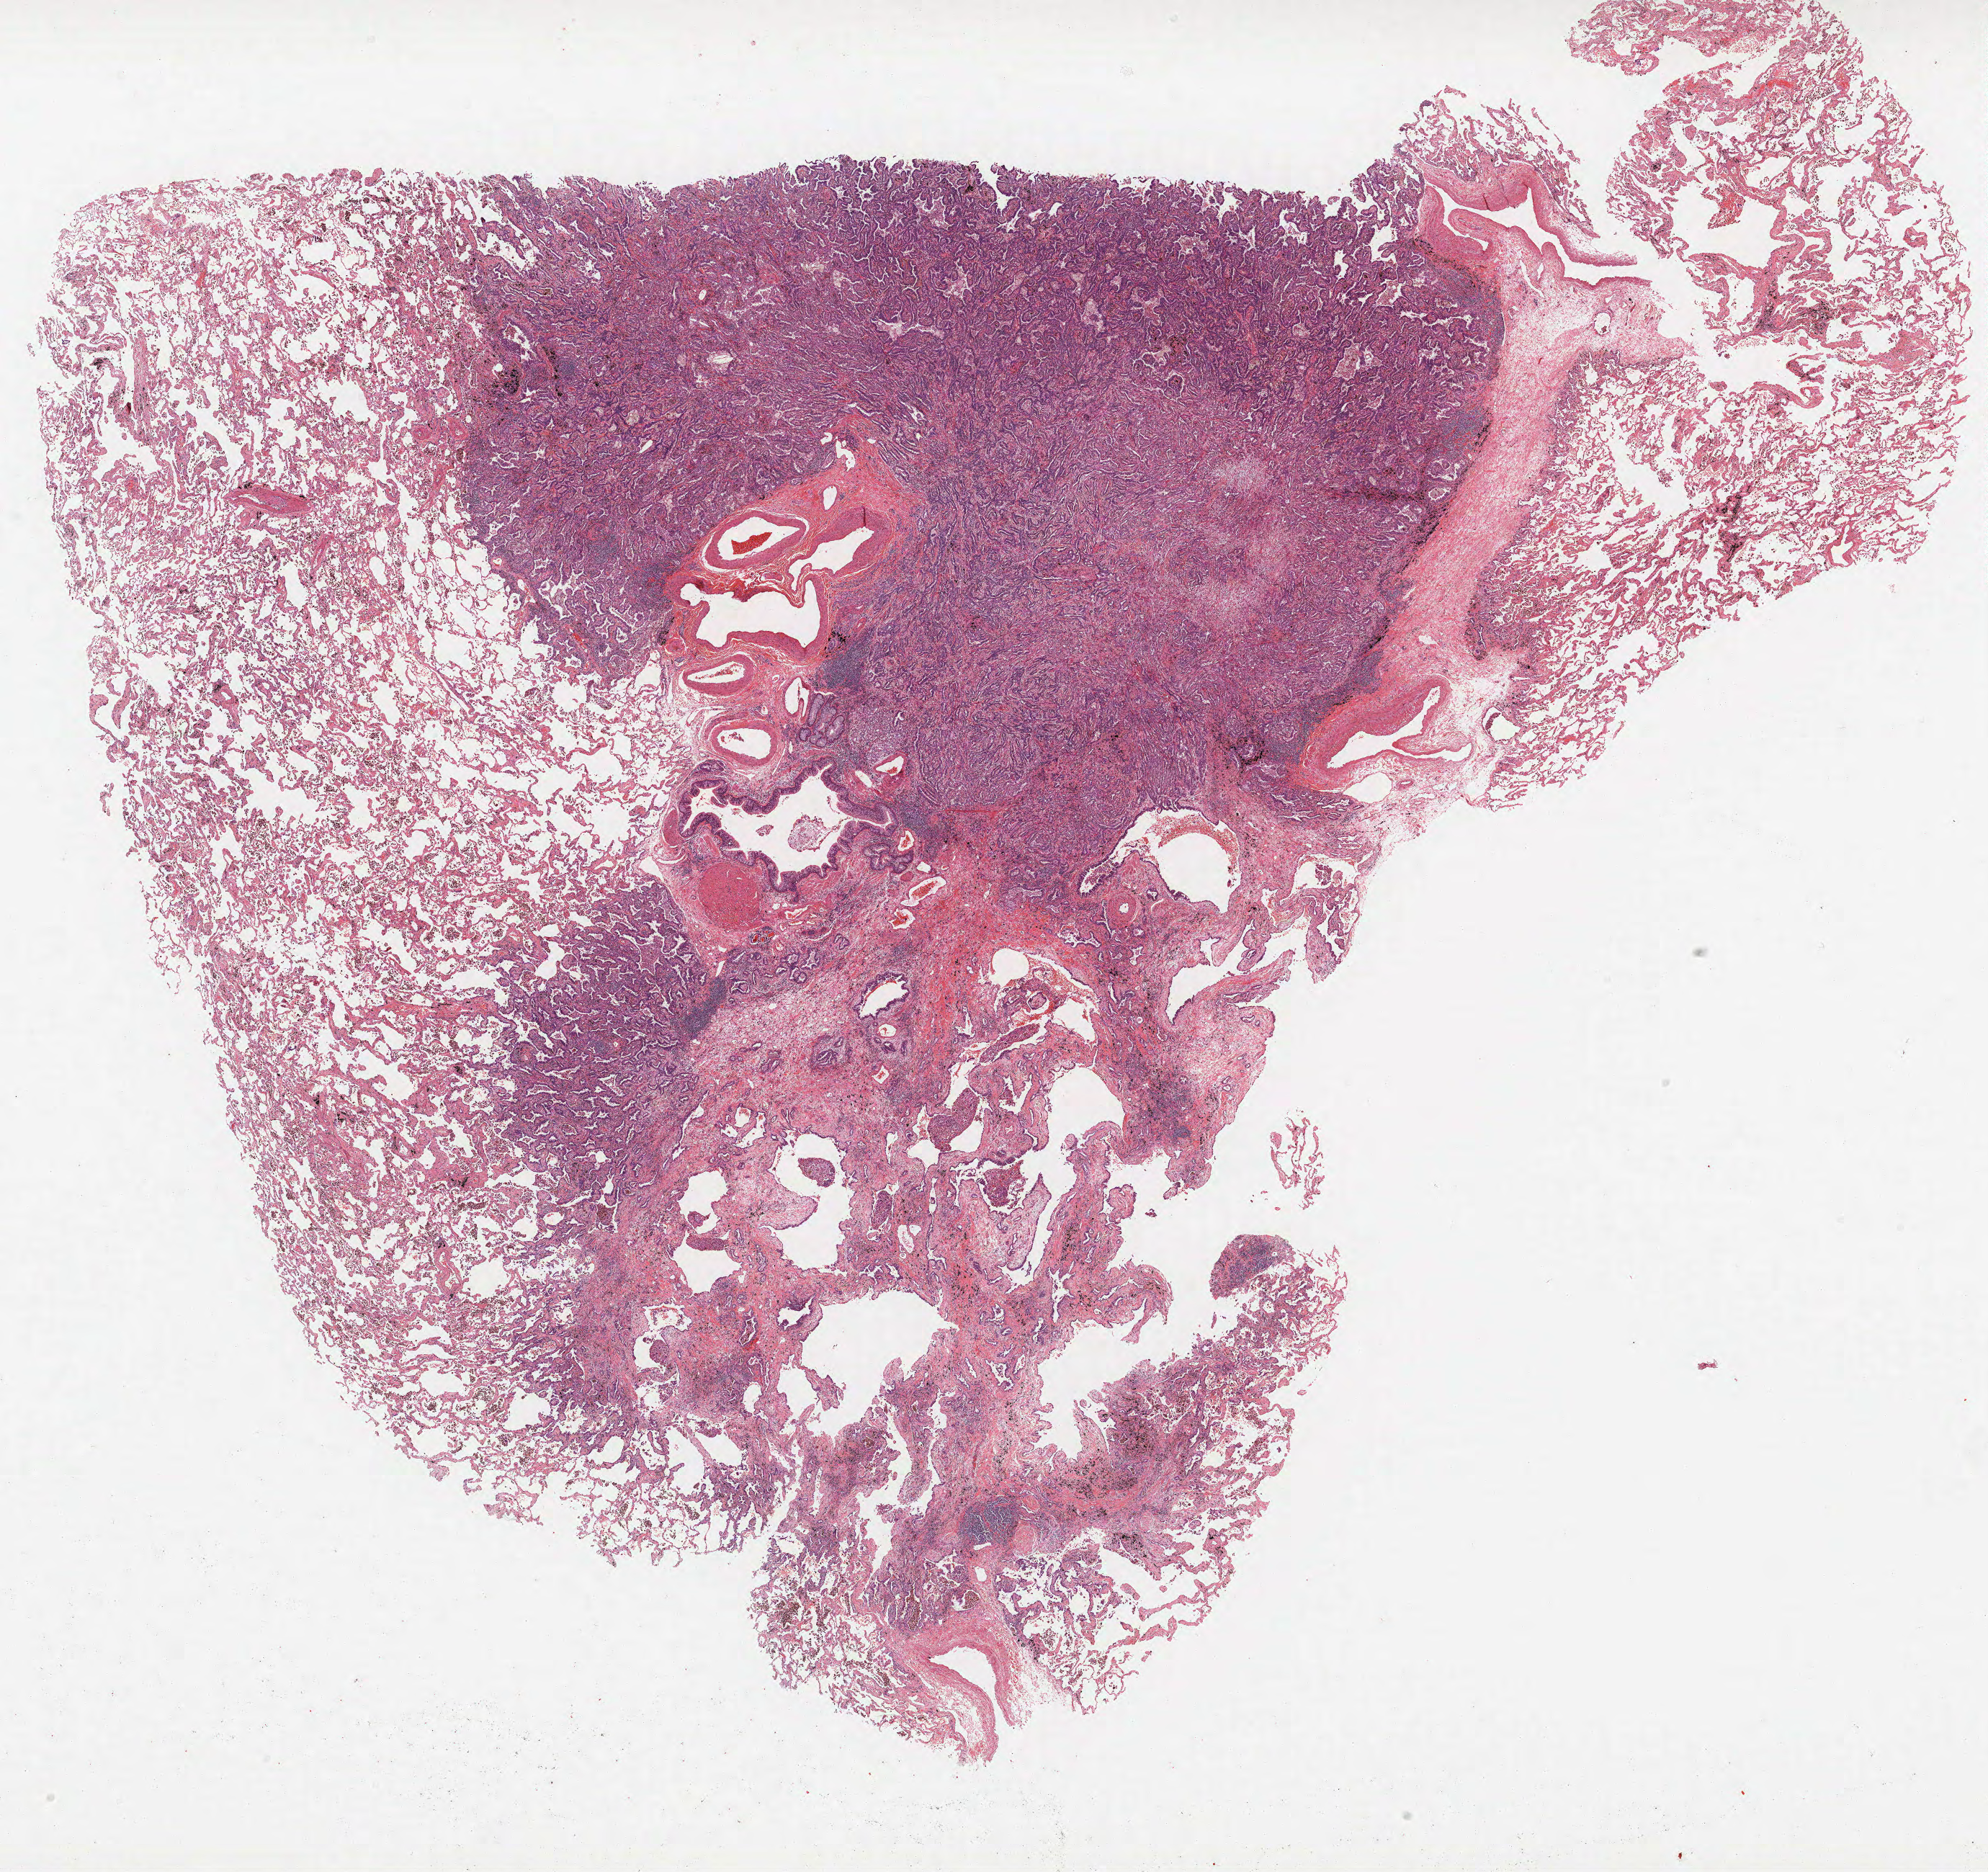
Whole-slide histology image, H&E-stained, a low-resolution overview of the entire scanned area, about 22.1 x 20.8 mm, FFPE section, lung tissue. Female patient, aged 61 at enrolment. Grade: moderately differentiated (G2).
• participant's lung-cancer diagnosis: Adenocarcinoma, NOS (ICD-O-3 8140/3)
• primary tumour location (clinical record): right upper lobe
• tumour size (pathology): 20 mm
• ICD-O-3 topography: upper lobe of lung (C34.1)
• stage (AJCC 6th edition): IA